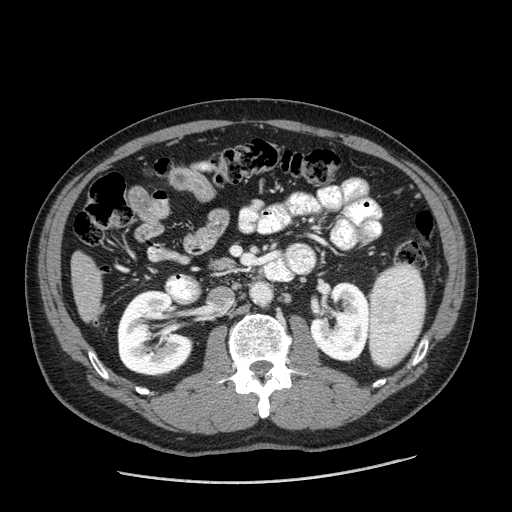
Contrast-enhanced abdominal CT (liver protocol), one axial slice. Position 53 of 198 along the scan axis. Reconstruction kernel STANDARD. One of 2 acquisitions stored at this slice position. Soft-tissue window (W 400 / L 40 HU). 2.5 mm slice thickness. 512 × 512 image matrix, field of view 400 × 400 mm. From the clinical record (not read from this slice): diagnosis: hepatocellular carcinoma (patient treated with transarterial chemoembolisation; whether this scan precedes or follows treatment is not stated here); TNM stage (as recorded): Stage-II; Child-Pugh class: A; tumour differentiation: moderately differentiated; tumour nodularity: multinodular.
Outlined on this slice (semi-automatically segmented with operator editing):
- liver parenchyma outside the tumour (the mass and vessels are separate outlines, so this box may not span the whole liver): box from (x=70, y=252) to (x=102, y=321) px